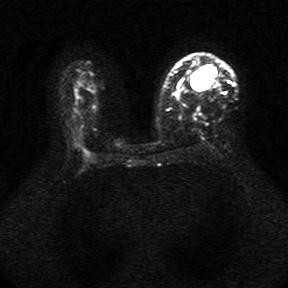
Breast MRI, one axial slice; diffusion-weighted series; image 2 of 4 stored at this slice position (different b-values; order by instance number); 1.5 T; 5 mm slice thickness; 288 × 288 image matrix, field of view 340 × 340 mm. Female patient.
Annotated regions visible in this slice (expert manual segmentation):
- tumour on diffusion-weighted imaging: bounding box <191,68,208,90> (left, top, right, bottom; pixels)